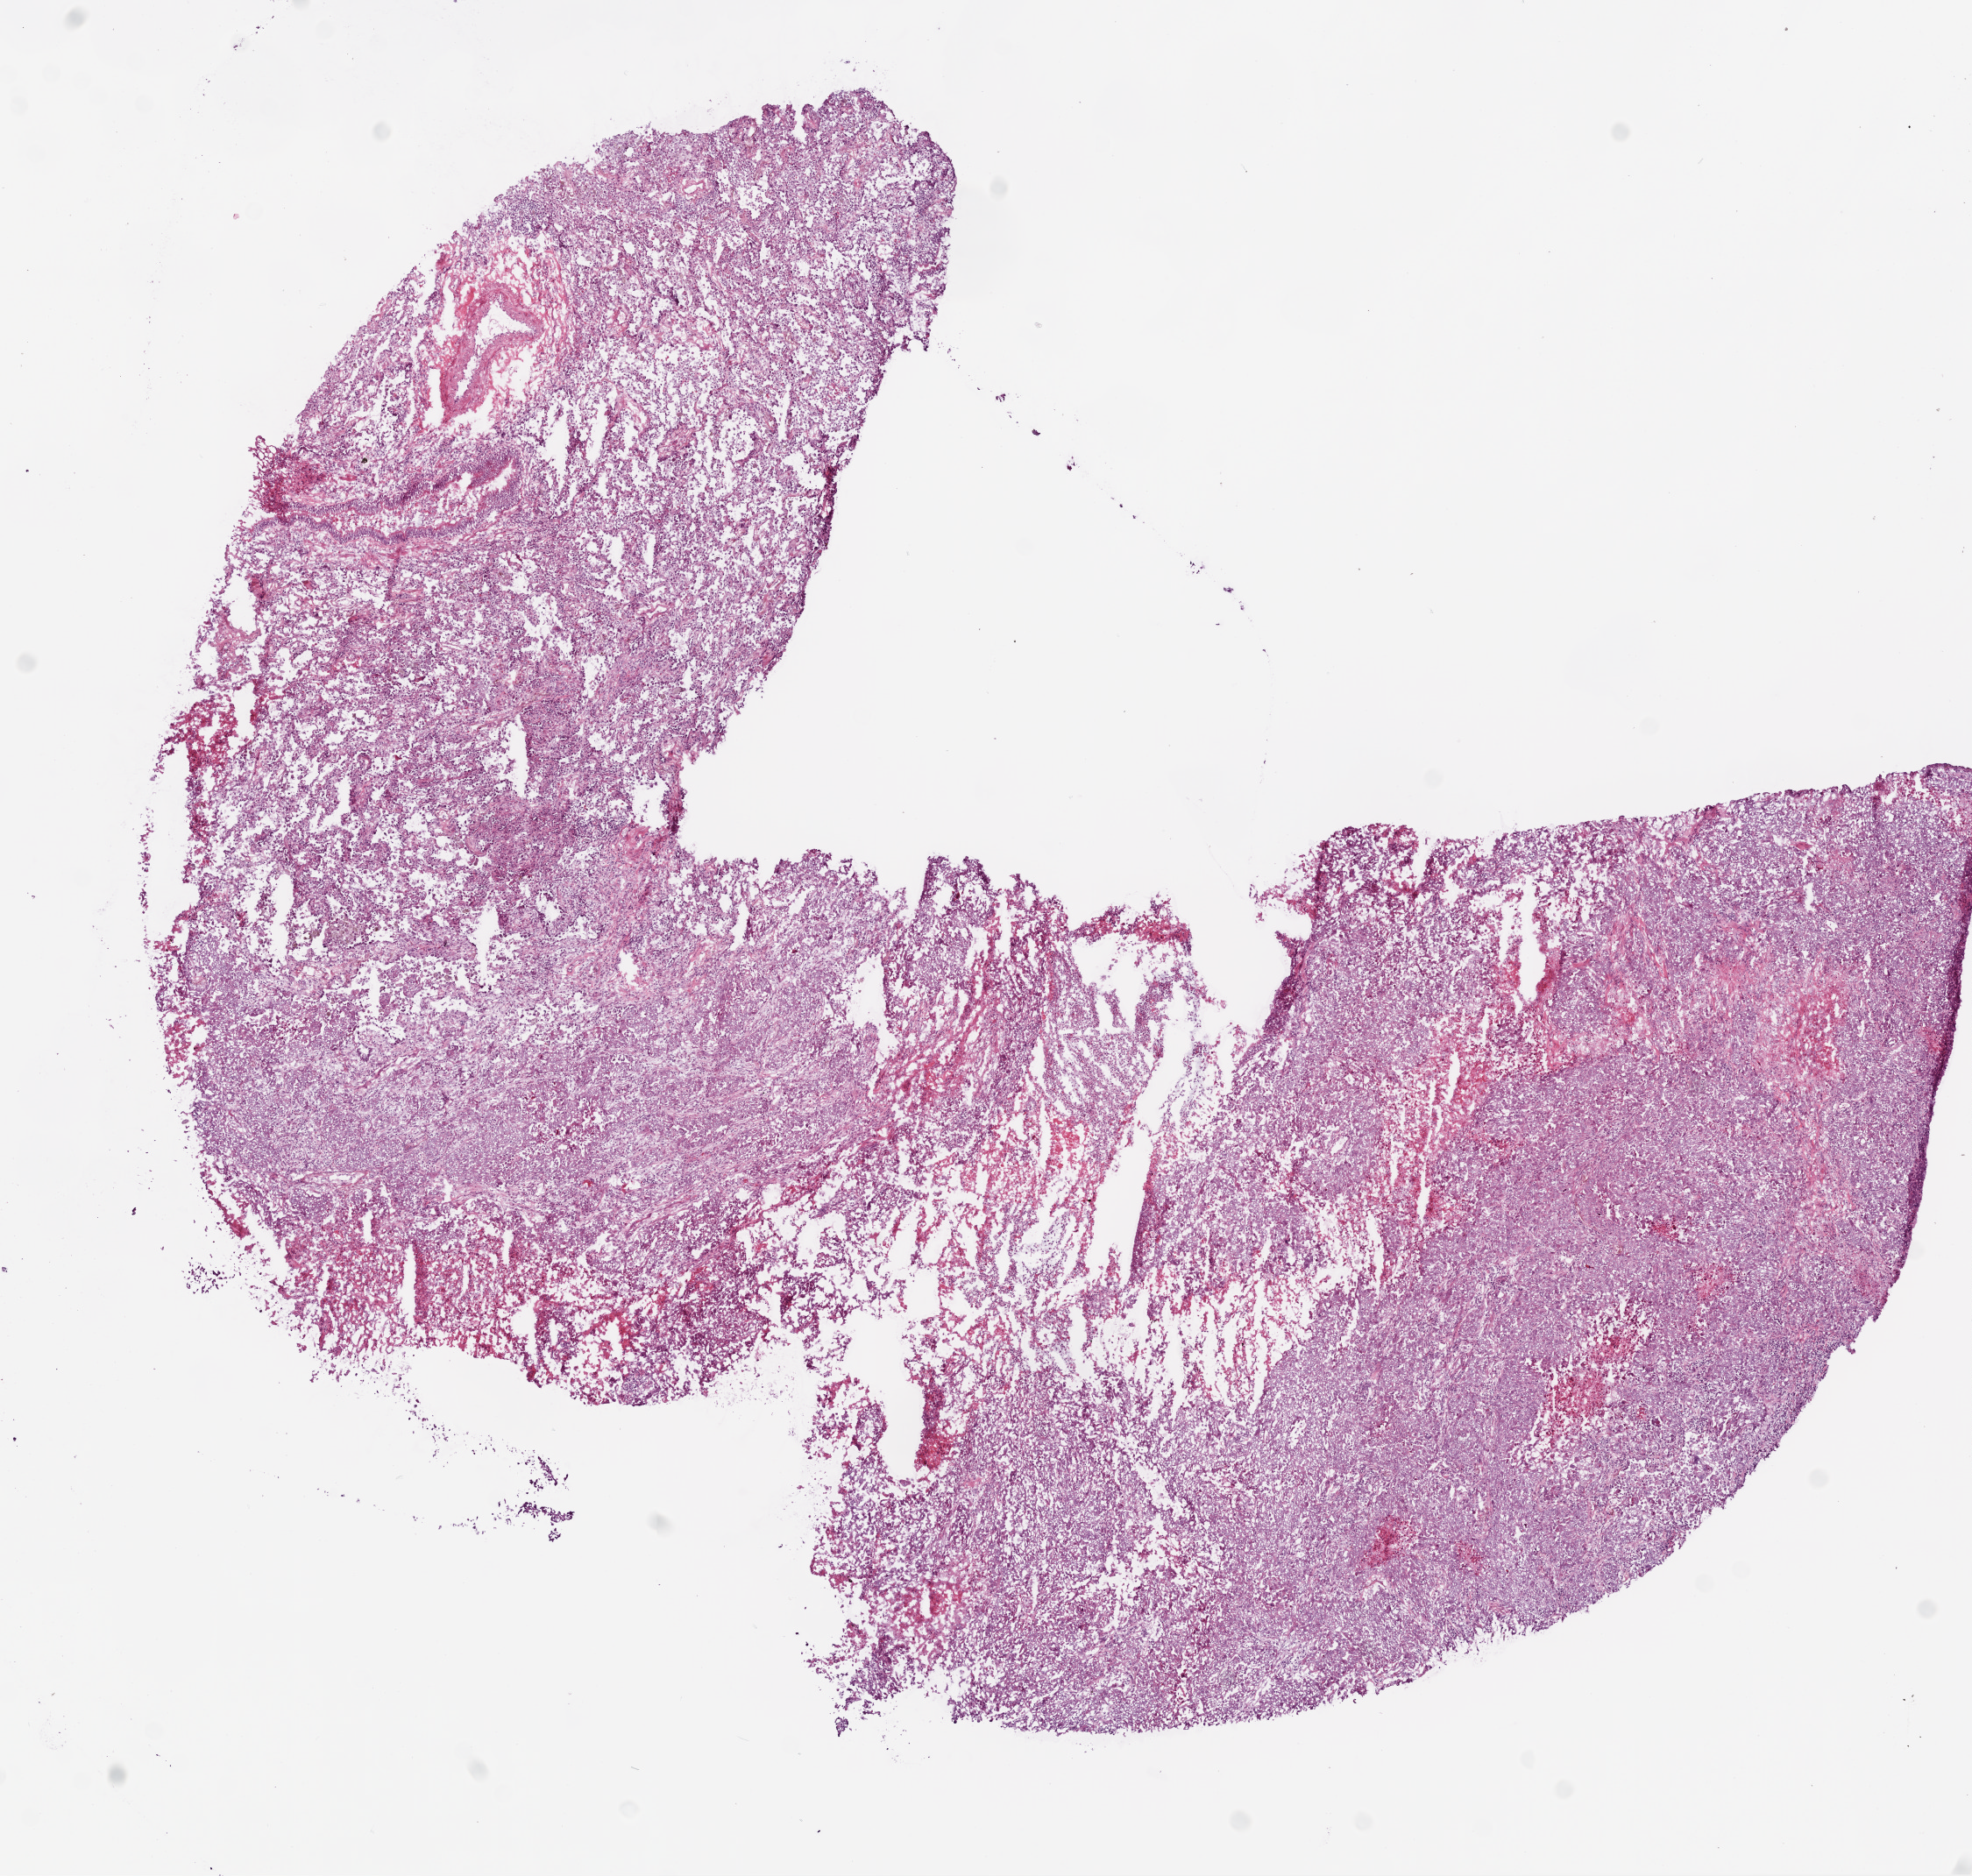
Digitized Hematoxylin and eosin (H&E) stained tissue section (whole slide) — whole scanned area (about 9.0 x 8.6 mm) shown as a low-resolution overview; frozen section from the bottom of the tissue portion; lung, primary tumour sample. Patient sex: female. Composition of this section per pathologist review: tumour cells 45%, tumour nuclei 60%, normal cells 45%, stromal cells 5%, necrosis 10%.
AJCC pathologic stage: IIIA. TNM: T3 N2 M0. Pathologic diagnosis: Papillary adenocarcinoma, NOS (upper lobe, lung).